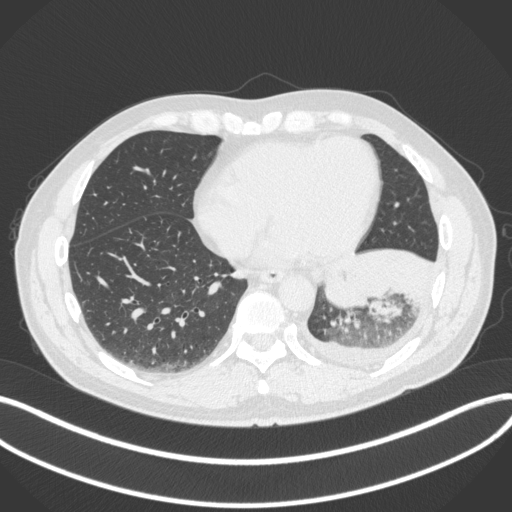
Chest CT, one axial slice. Slice 116 of 350 in the series (ordered by position). 120 kVp. Lung window (W 1500 / L -600 HU). 1 mm slice thickness. 512 × 512 image matrix, field of view 400 × 400 mm. Male patient, age 58 years. From the clinical record (not read from this slice): clinical TNM (as recorded): T3 N1 M1b; histopathological grade: G3.
Outlined on this slice (bounding box drawn by a radiologist):
- lung tumour (recorded histology: small cell carcinoma): bounding box <320,265,372,313> (left, top, right, bottom; pixels)